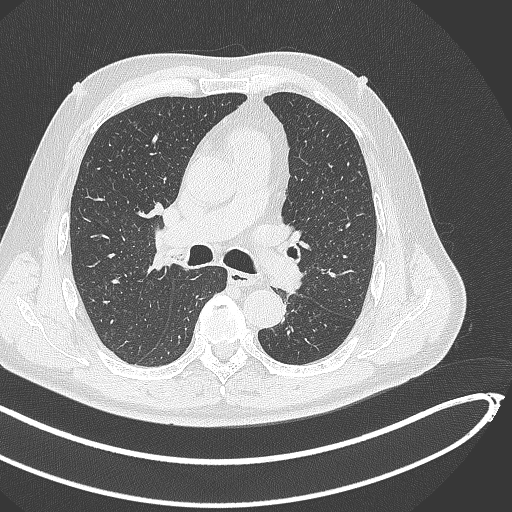
Chest CT, one axial slice; position 282 of 468 along the scan axis; reconstruction kernel B70f; lung window (W 1500 / L -600 HU); 1 mm slice thickness; 512 × 512 image matrix. Patient: male, 64 years. Case-level facts recorded for this patient, not image findings: clinical TNM (as recorded): T1c N0 M0; histopathological grade: G2.
Structures marked on this image (bounding box drawn by a radiologist):
- lung tumour (recorded histology: squamous cell carcinoma): bounding box [x1, y1, x2, y2] px = [263, 259, 308, 295]